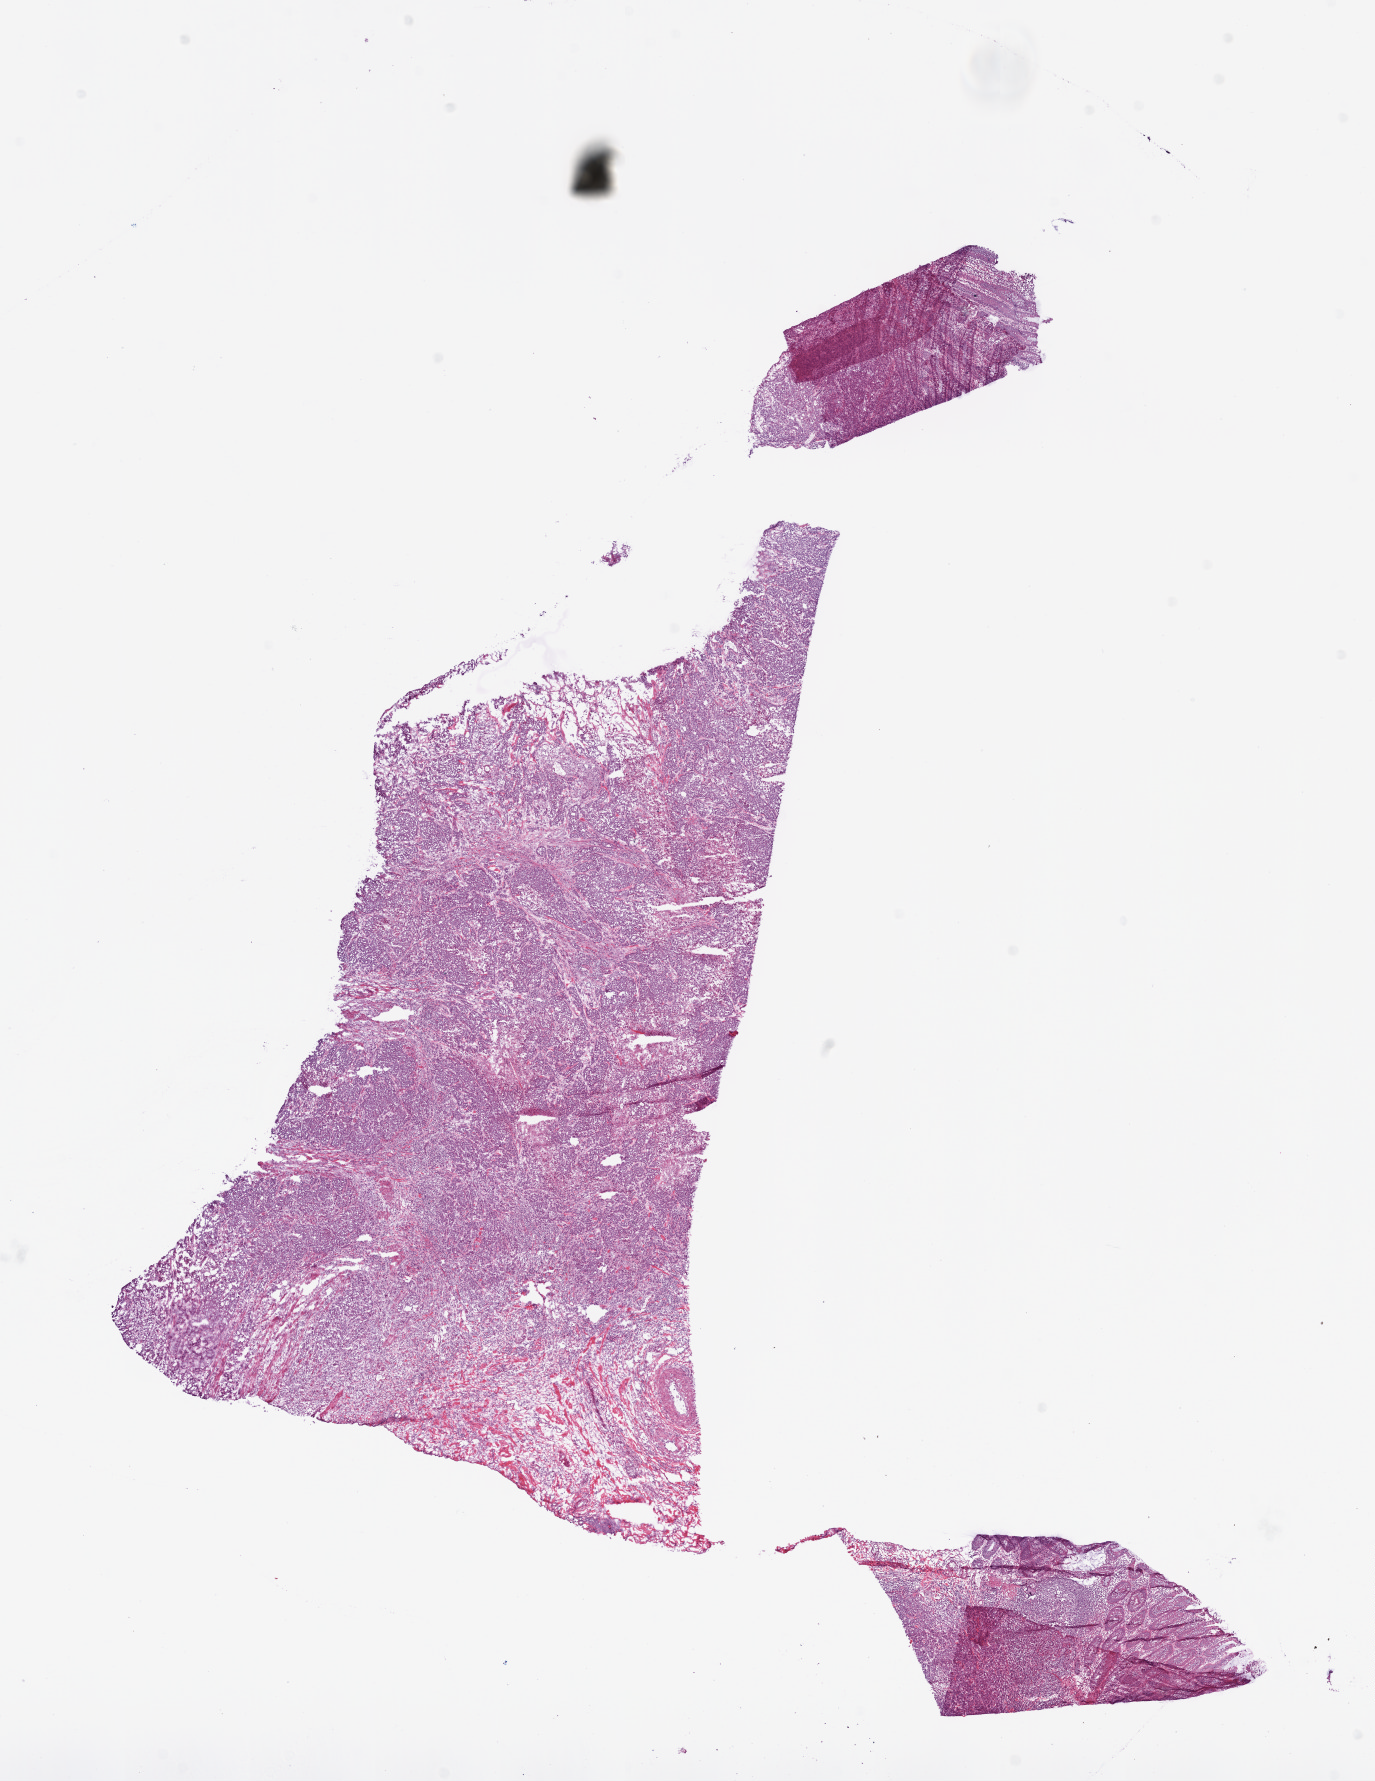
Whole-slide histology image, H&E — a low-resolution overview of the entire scanned area, about 11.0 x 14.3 mm (slide scanned at 20x). Frozen section from the bottom of the tissue portion. Sample: primary tumour, colon. Female patient; age at initial diagnosis 86 years. Pathologist review of this section (percent, as recorded): tumour cells 85%, tumour nuclei 85%.
Histologic diagnosis: Adenocarcinoma, NOS (ascending colon).